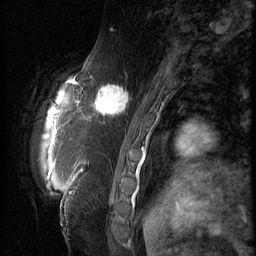
Breast MRI (dynamic contrast-enhanced), one sagittal slice; position 18 of 66 along the scan axis; 3 images stored at this slice position (order not interpretable as contrast timing); 1.5 T; TE 4.2 ms, TR 9 ms; 2.5 mm slice thickness; 256 × 256 image matrix, field of view 180 × 180 mm. Female patient, age 57 years. From the clinical record (not read from this slice): setting: breast cancer imaged before/during neoadjuvant chemotherapy; receptor status: triple-negative.
Annotated regions visible in this slice (semi-automatically segmented with operator editing):
- analysis volume of interest (the breast-tissue region the enhancement analysis was run in; not a lesion): box from (x=86, y=74) to (x=138, y=129) px
- tumour enhancement mask (voxels above the 140 % enhancement threshold inside the analysis volume of interest): (x=91, y=85)–(x=129, y=116)